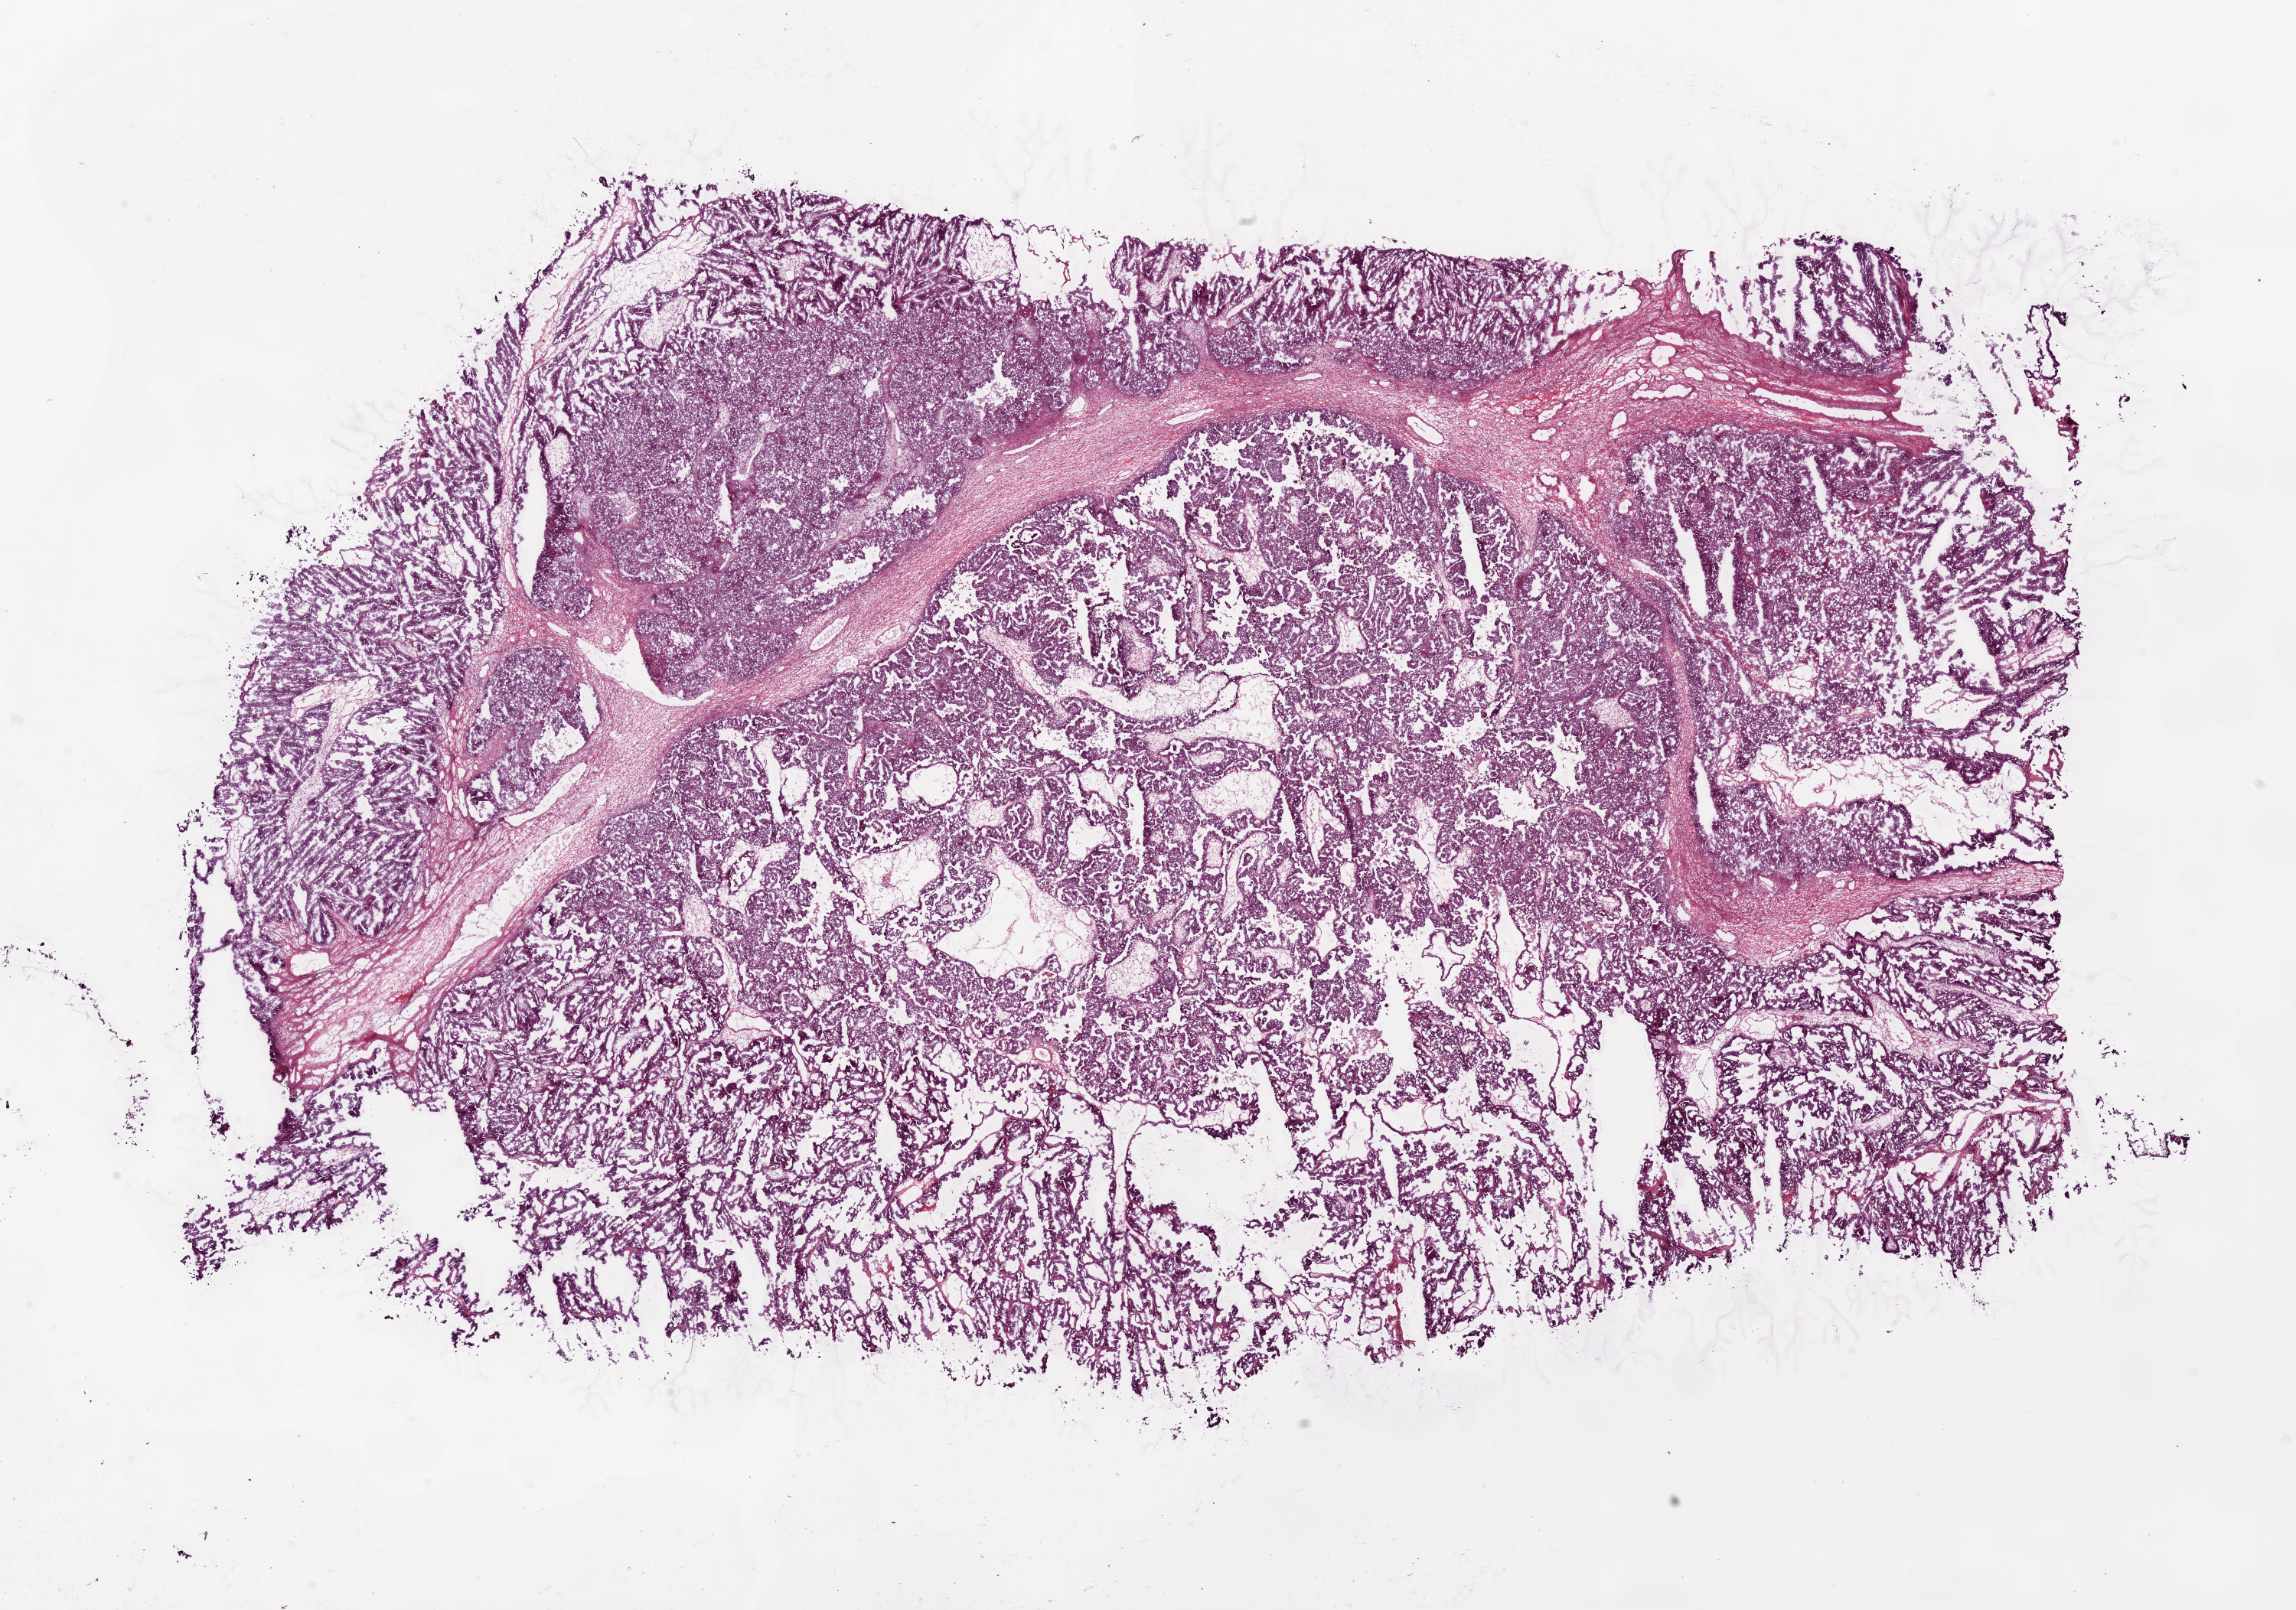
Whole-slide histology image, H&E-stained, a low-resolution overview of the entire scanned area, about 24.1 x 16.9 mm, frozen section from the bottom of the tissue portion, primary tumour sample from the ovary. Female patient; age at initial diagnosis 50 years. Histologic grade: G3 (poorly differentiated). Slide review estimates, as recorded: tumour cells 90%, tumour nuclei 85%, normal cells 0%, stromal cells 10%, necrosis 0%. Inflammatory infiltration, as recorded: lymphocyte infiltration 5%, monocyte infiltration 2%, neutrophil infiltration 0%.
Laterality: bilateral. Histologic diagnosis: Serous cystadenocarcinoma, NOS. FIGO stage: IIIC.